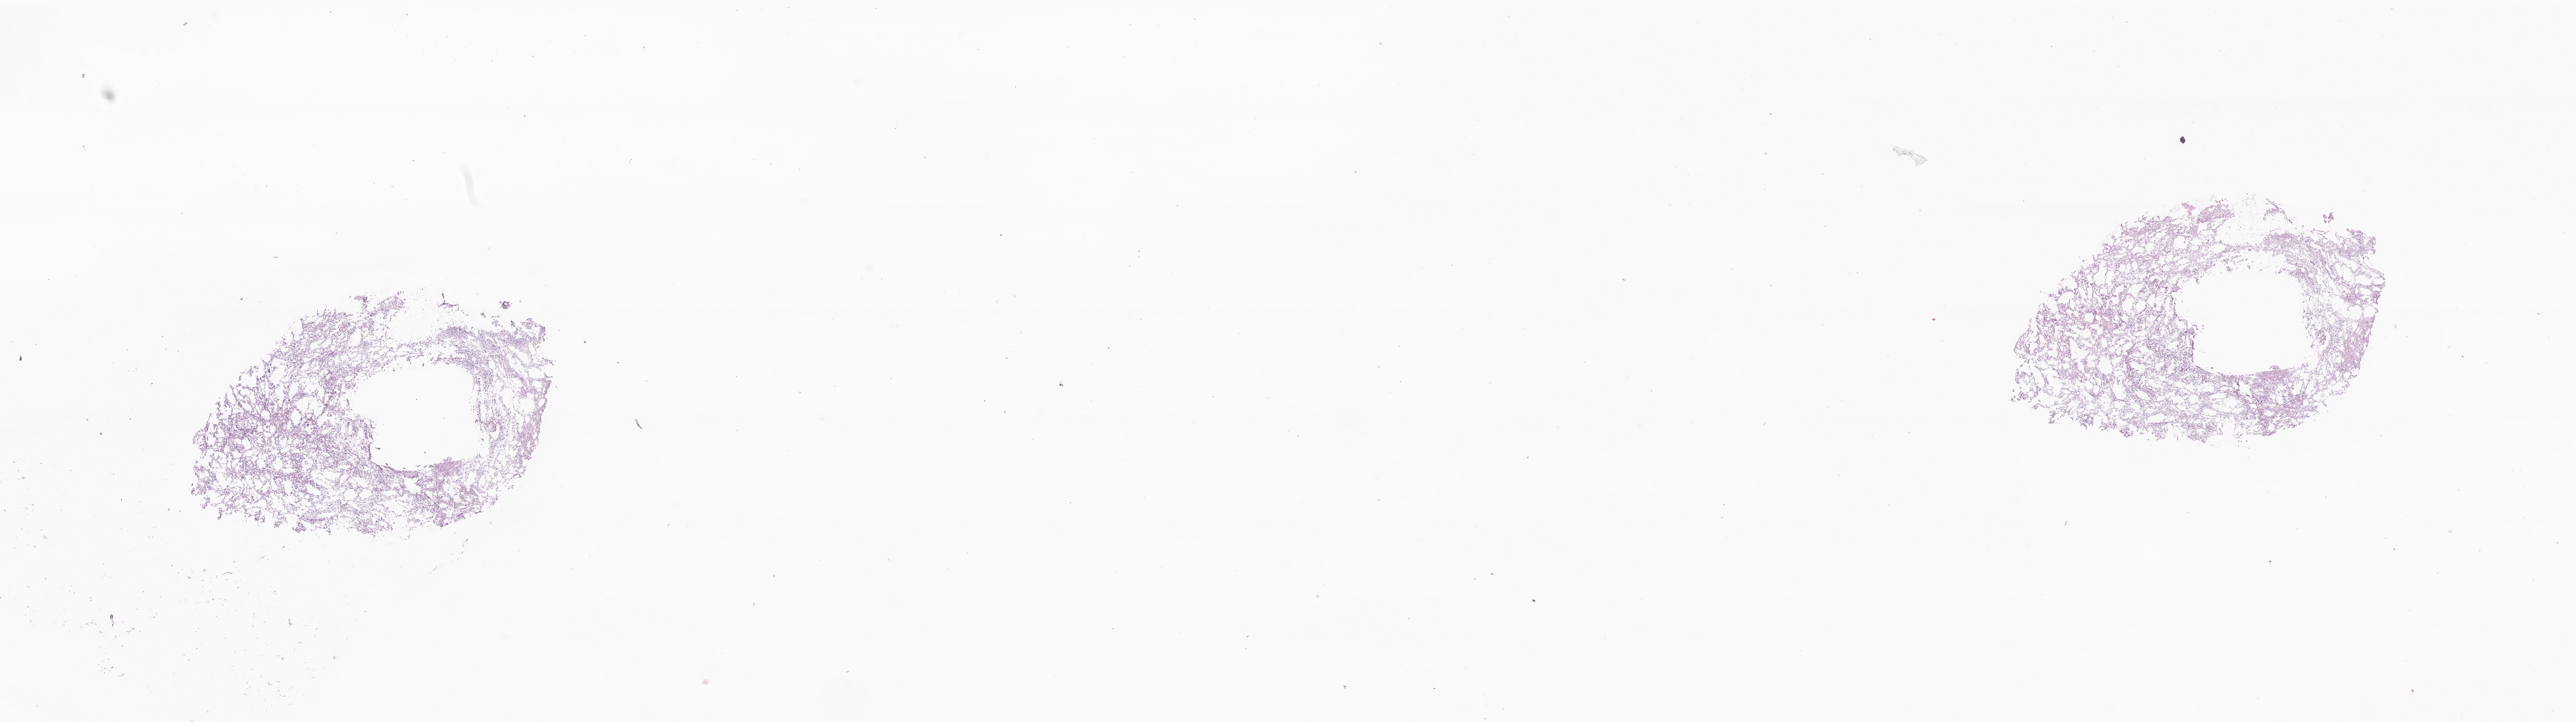
H&E whole-slide image of tumor tissue from the cerebellum, shown as a low-resolution overview of the whole scanned area (about 26.2 x 7.4 mm). Cryosection (OCT / tissue freezing medium). Male patient, age 183 months (15 years 3 months).
Diagnosis (ICD-O-3 morphology term): Pilocytic astrocytoma.